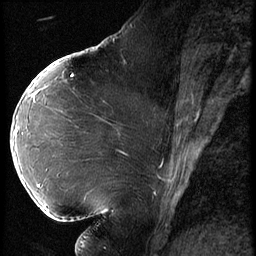
Breast MRI (dynamic contrast-enhanced), one sagittal slice. Slice 30 of 62 in the series (ordered by position). 3 images stored at this slice position (order not interpretable as contrast timing). 1.5 T. TE 4.2 ms, TR 9 ms. 256 × 256 image matrix, field of view 180 × 180 mm. Patient: female, 43 years. Case-level facts recorded for this patient, not image findings: setting: breast cancer imaged before/during neoadjuvant chemotherapy; receptor status: HER2-positive.
Structures marked on this image (semi-automatic segmentation, software-assisted and operator-edited):
- analysis volume of interest (the breast-tissue region the enhancement analysis was run in; not a lesion): bounding box [x1, y1, x2, y2] px = [11, 90, 82, 203]
- tumour enhancement mask (voxels above the 140 % enhancement threshold inside the analysis volume of interest): [15, 92, 40, 186]